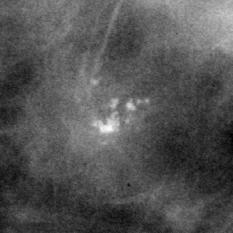
Crop from a digitized film mammogram around one marked abnormality; left breast; CC view; BI-RADS breast density category 3 (scale 1–4).
- Finding: calcifications, morphology pleomorphic, distribution clustered / segmental; BI-RADS assessment category 4; pathology result (as recorded, not read from the image): benign.